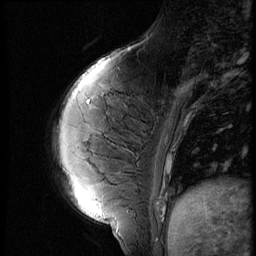
Breast MRI (dynamic contrast-enhanced), one sagittal slice; position 17 of 56 along the scan axis; 3 images stored at this slice position (order not interpretable as contrast timing); 1.5 T; TE 4.2 ms, TR 9 ms; 2.5 mm slice thickness; 256 × 256 image matrix, field of view 180 × 180 mm. Patient: female, 35 years. From the clinical record (not read from this slice): setting: breast cancer imaged before/during neoadjuvant chemotherapy; receptor status: HR-positive, HER2-negative.
Structures marked on this image (semi-automatically segmented with operator editing):
- analysis volume of interest (the breast-tissue region the enhancement analysis was run in; not a lesion): box from (x=58, y=70) to (x=171, y=208) px
- tumour enhancement mask (voxels above the 140 % enhancement threshold inside the analysis volume of interest): (x=168, y=161)–(x=171, y=173)